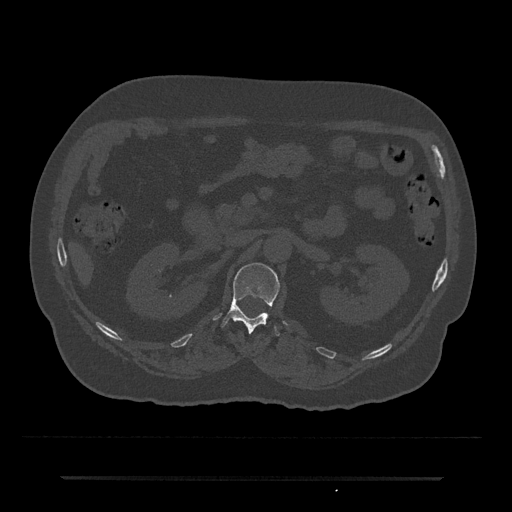
CT including the spine, one axial slice. Slice 71 of 797 in the series (ordered by position). Bone window (W 1800 / L 400 HU). 0.5 mm slice thickness. 512 × 512 image matrix, field of view 437 × 437 mm. Patient: male, 69 years. From the clinical record (not read from this slice): primary cancer: prostate.
Structures marked on this image (semi-automatic segmentation, software-assisted and operator-edited):
- L1 vertebra: bounding box (x1, y1, x2, y2) in pixels: (220, 263, 279, 336)